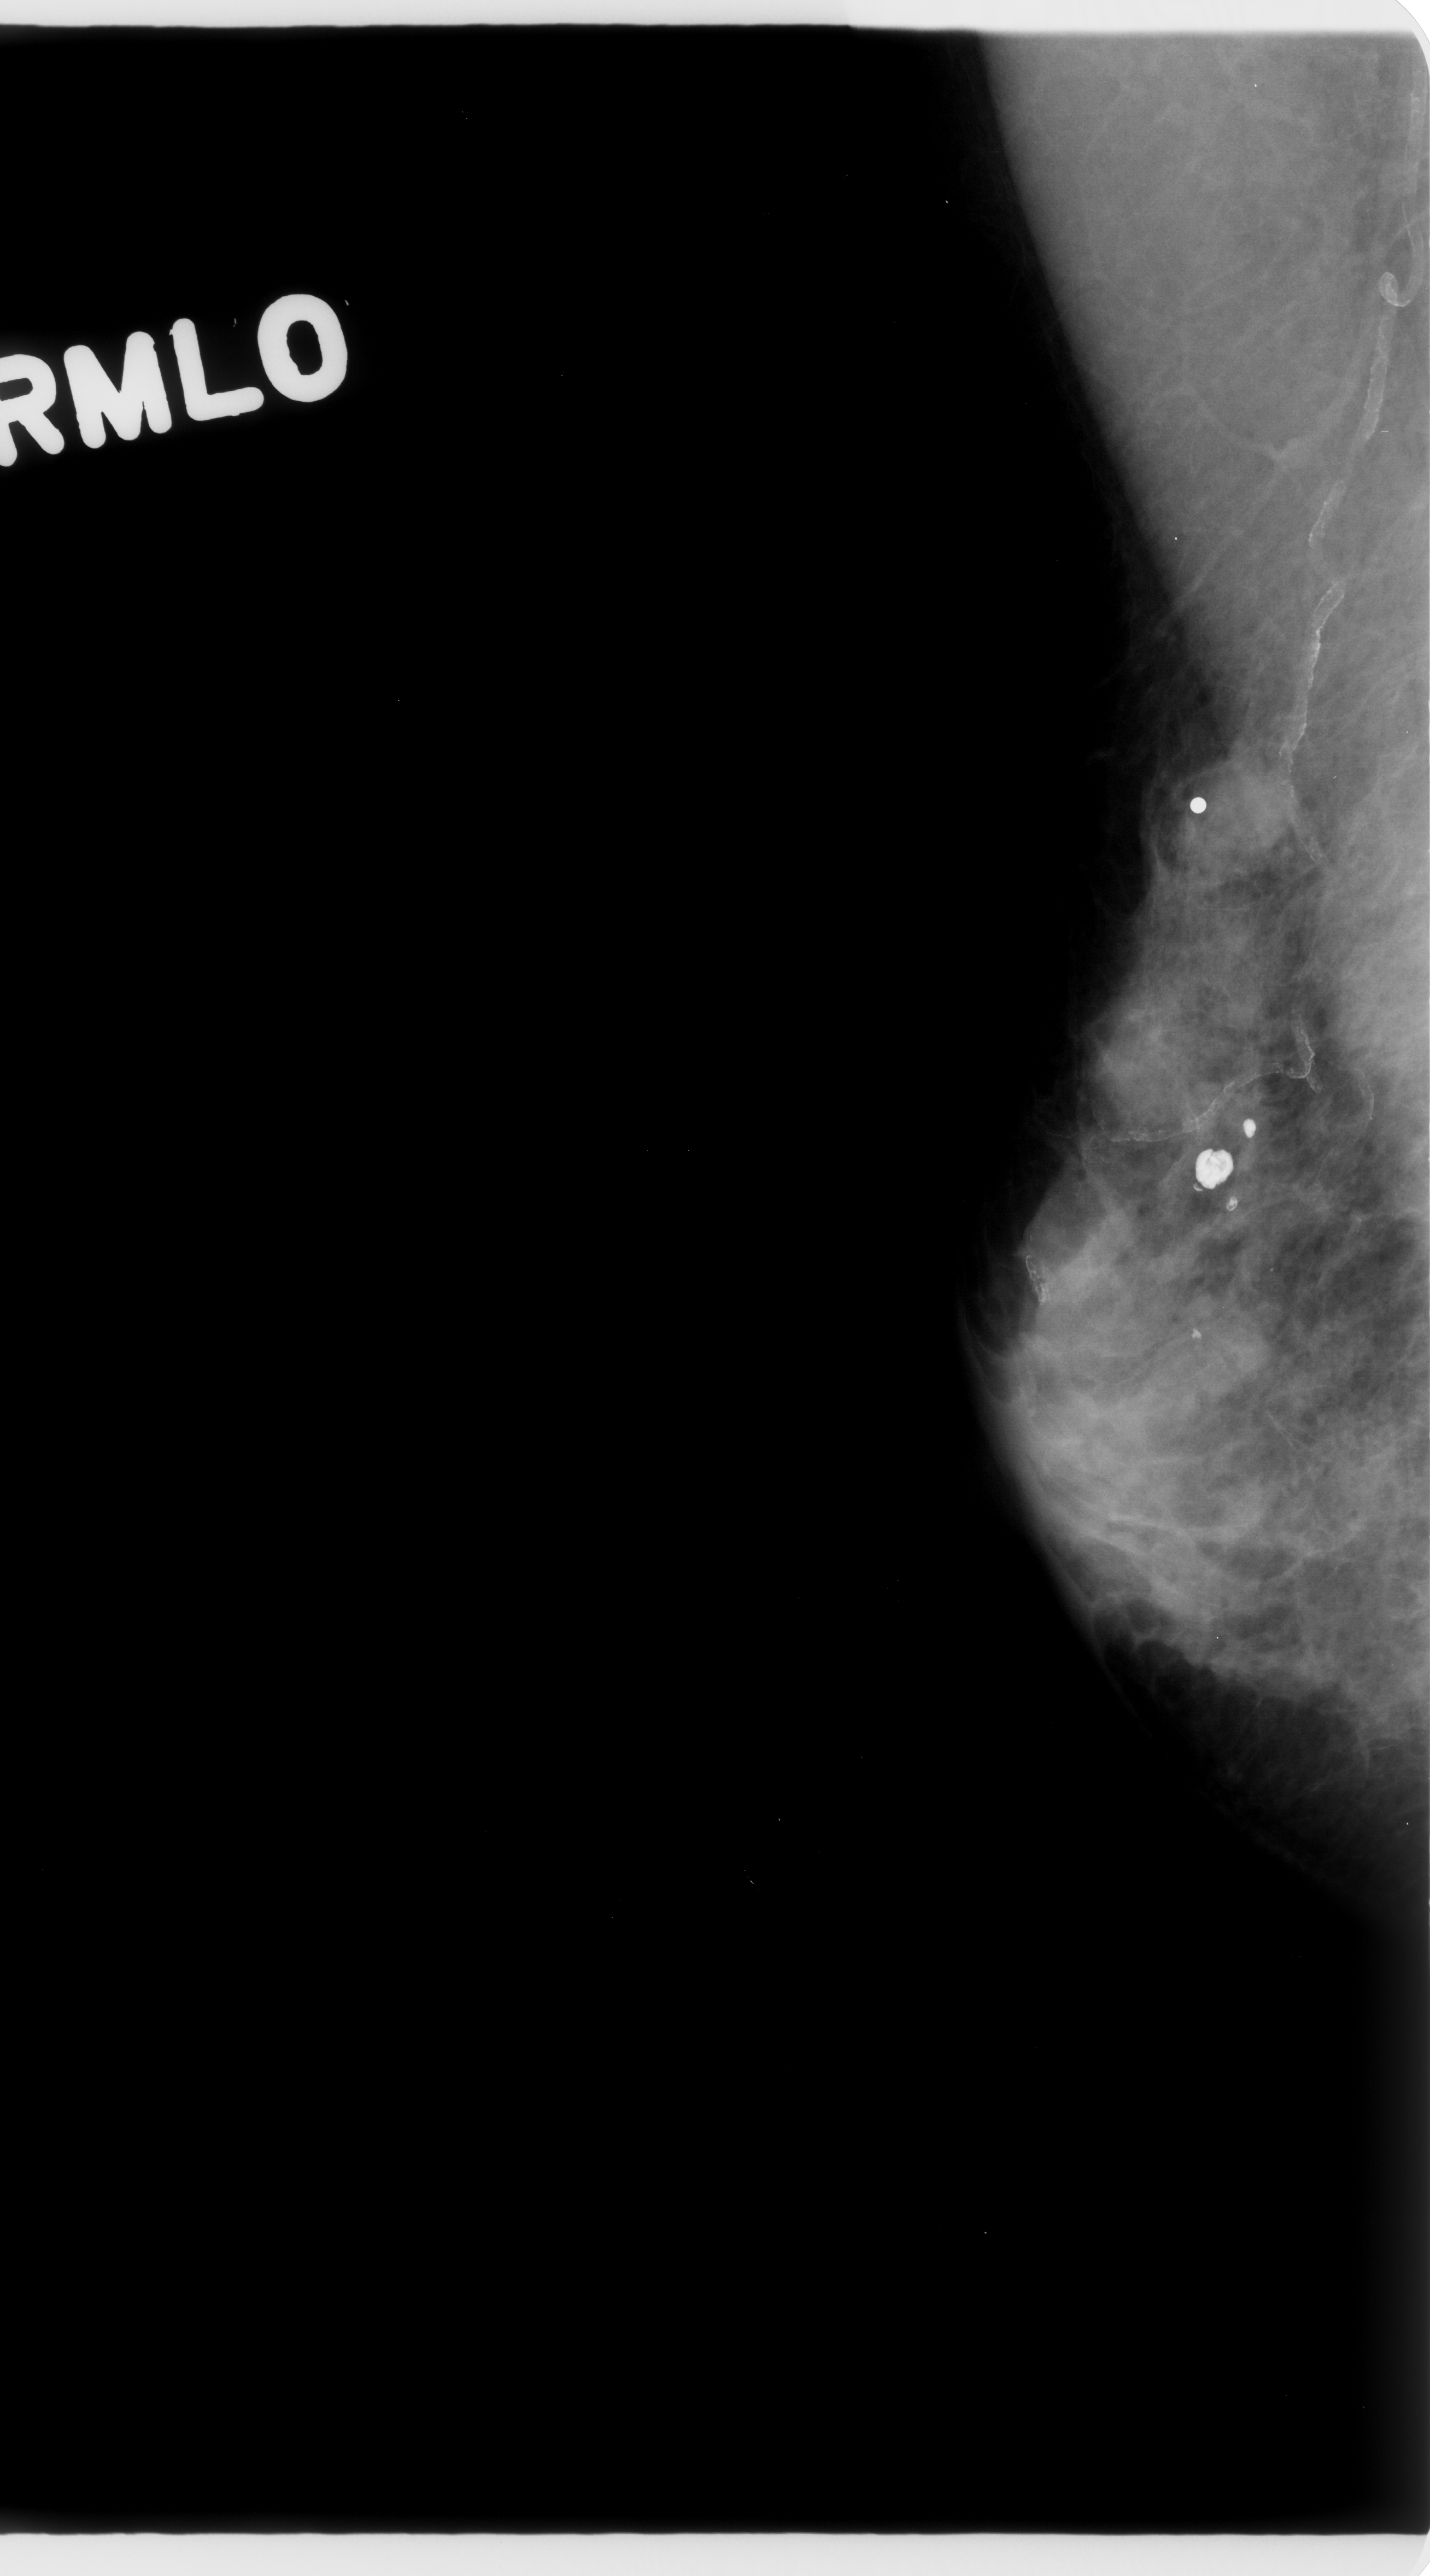
Mammogram (digitized film); right breast; mediolateral oblique (MLO) view; BI-RADS breast density category 3 (scale 1–4).
Radiologist-marked abnormalities on this image: mass, shape oval, margins circumscribed; BI-RADS assessment category 4; subtlety rating 4 on a 1 (subtle) to 5 (obvious) scale; pathology result (as recorded, not read from the image): malignant.